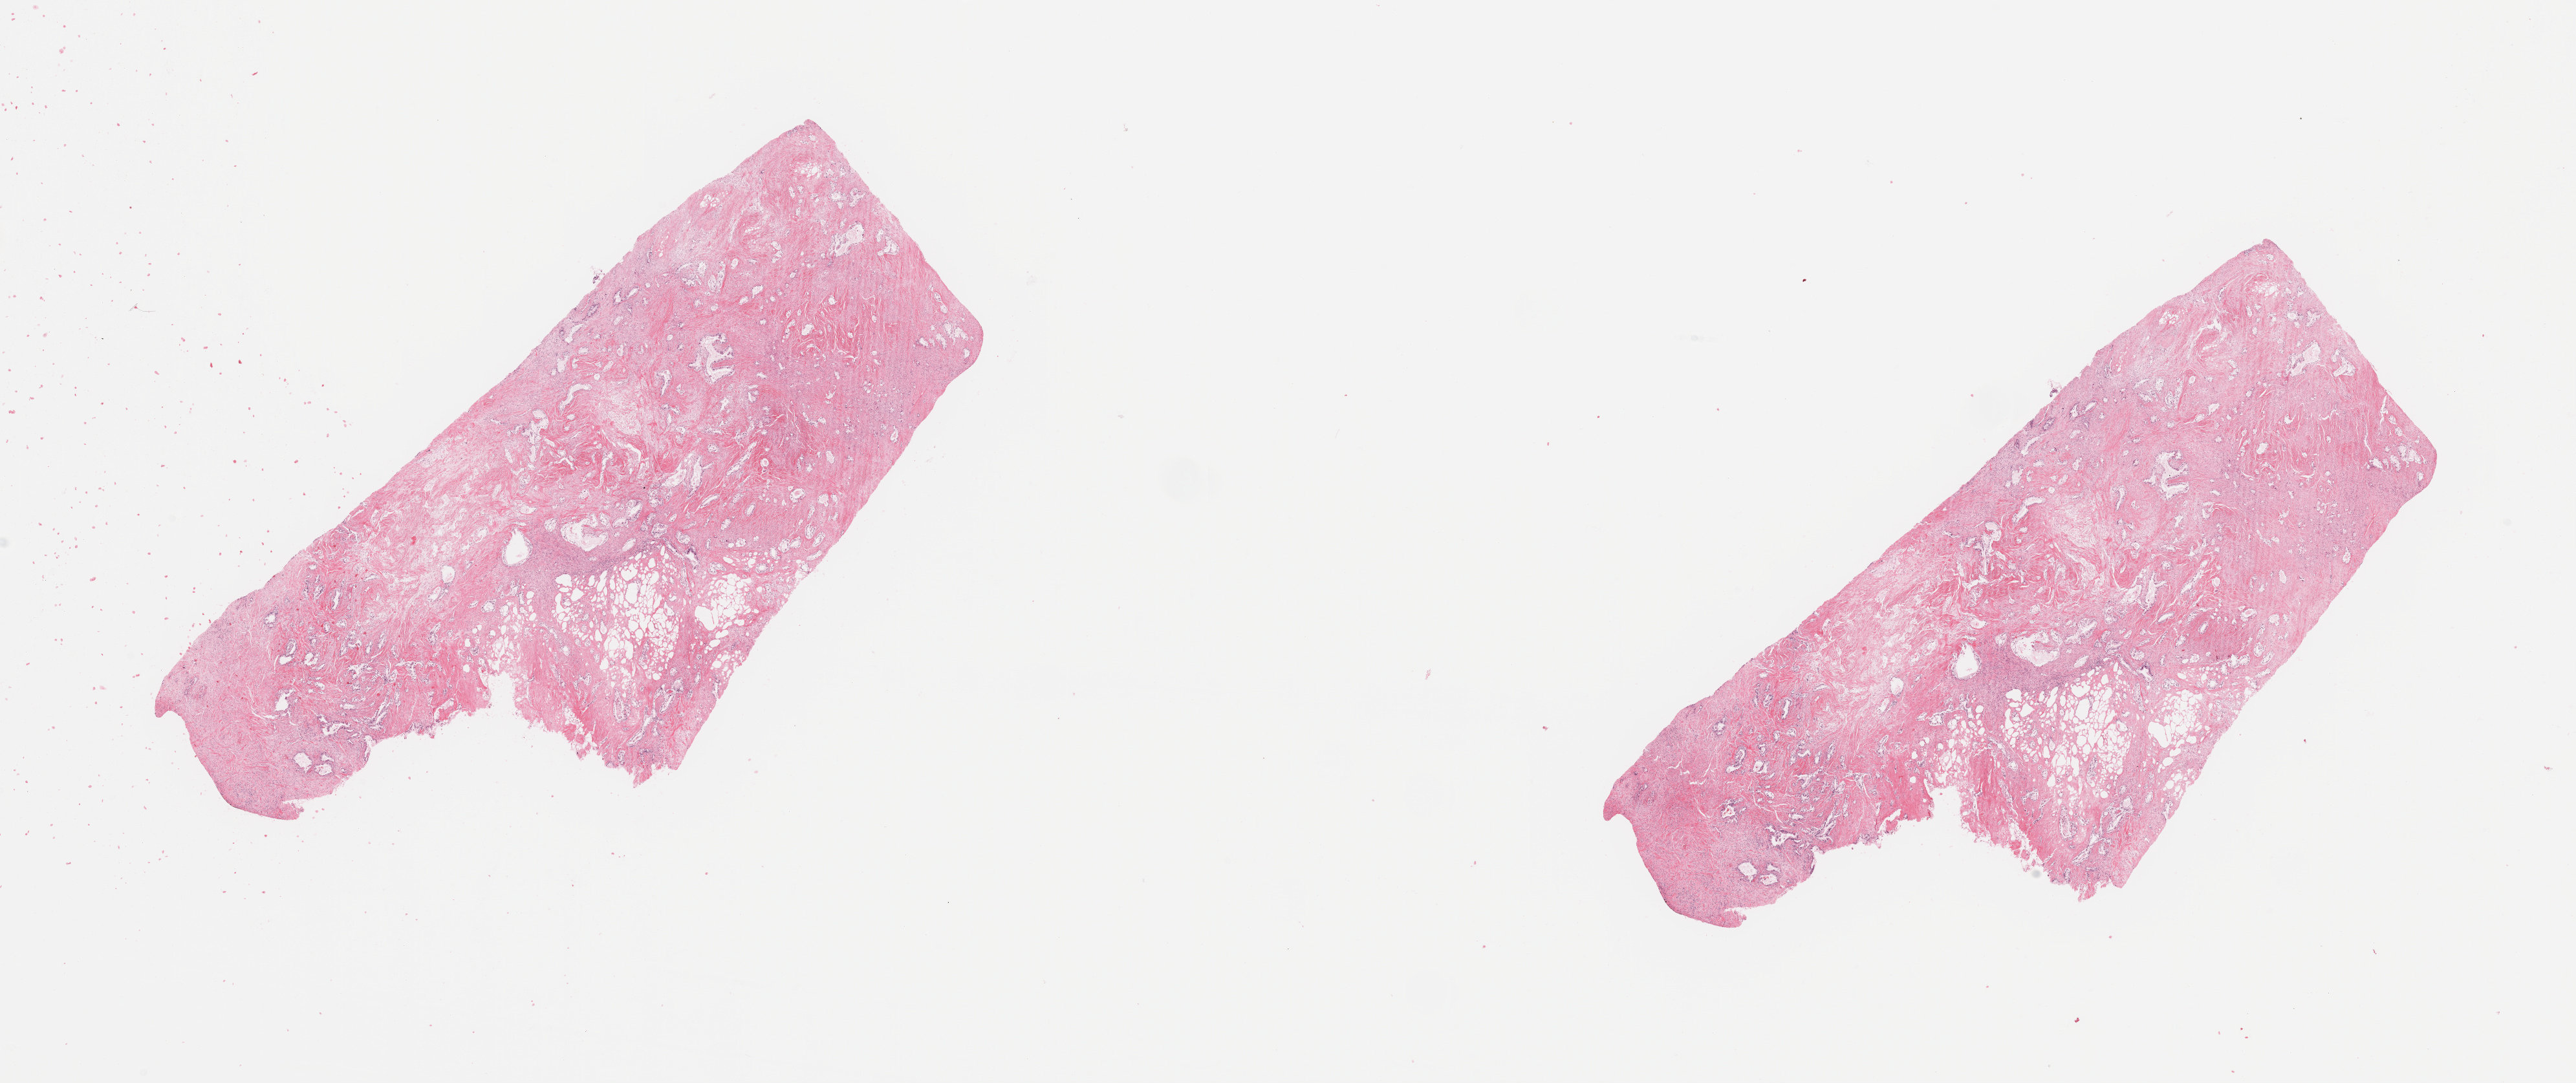
Digitized H&E tissue section (whole slide), low-resolution overview of the scanned area, about 31.5 x 13.2 mm. Tumour tissue sample, sampled site: pancreas. 78-year-old female patient. Histologic grade: G1 (well differentiated). Slide review estimates, as recorded: tumour nuclei 80%, necrosis 5%.
Diagnosis: Infiltrating duct carcinoma, NOS. Primary tumour site (as recorded): tail. AJCC pathologic stage: III.